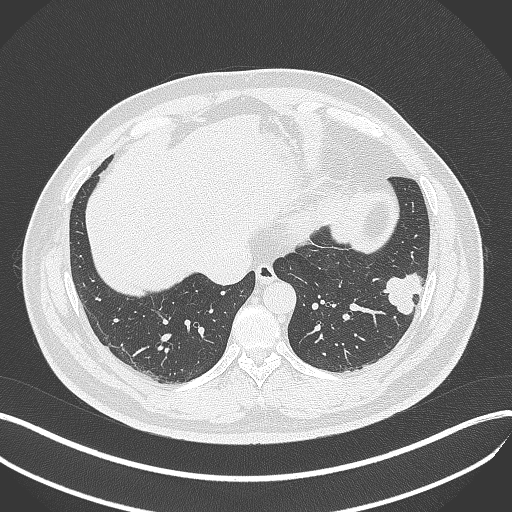
Chest CT, one axial slice. Position 123 of 429 along the scan axis. 120 kVp. Lung window (W 1500 / L -600 HU). 1 mm slice thickness. 512 × 512 image matrix, field of view 400 × 400 mm. Patient: male, 39 years. From the clinical record (not read from this slice): clinical TNM (as recorded): T2a N0 M0; histopathological grade: G2-3.
Outlined on this slice (rectangle marked by the reading radiologist):
- lung tumour (recorded histology: adenocarcinoma): bounding box (x1, y1, x2, y2) in pixels: (380, 273, 426, 319)